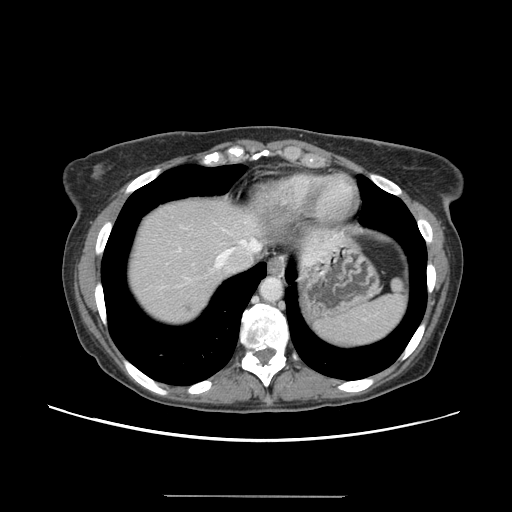
Contrast-enhanced abdominal CT, one axial slice. Slice 127 of 144 in the series (ordered by position). 120 kVp. Soft-tissue window (W 400 / L 40 HU). 2.5 mm slice thickness. 512 × 512 image matrix, field of view 380 × 380 mm. Female patient, age 53 years. Case-level facts recorded for this patient, not image findings: diagnosis: colorectal cancer liver metastases, imaged before liver resection; multiple liver metastases: yes; largest metastasis: 1.1 cm; chemotherapy before resection: no.
Structures marked on this image (manually delineated by an expert):
- hepatic veins: bounding box (x1, y1, x2, y2) in pixels: (215, 239, 262, 268)
- liver: (127, 199, 263, 323)
- planned liver remnant (the part of the liver to remain after resection): (127, 196, 262, 293)
- liver metastasis: (185, 305, 192, 312)